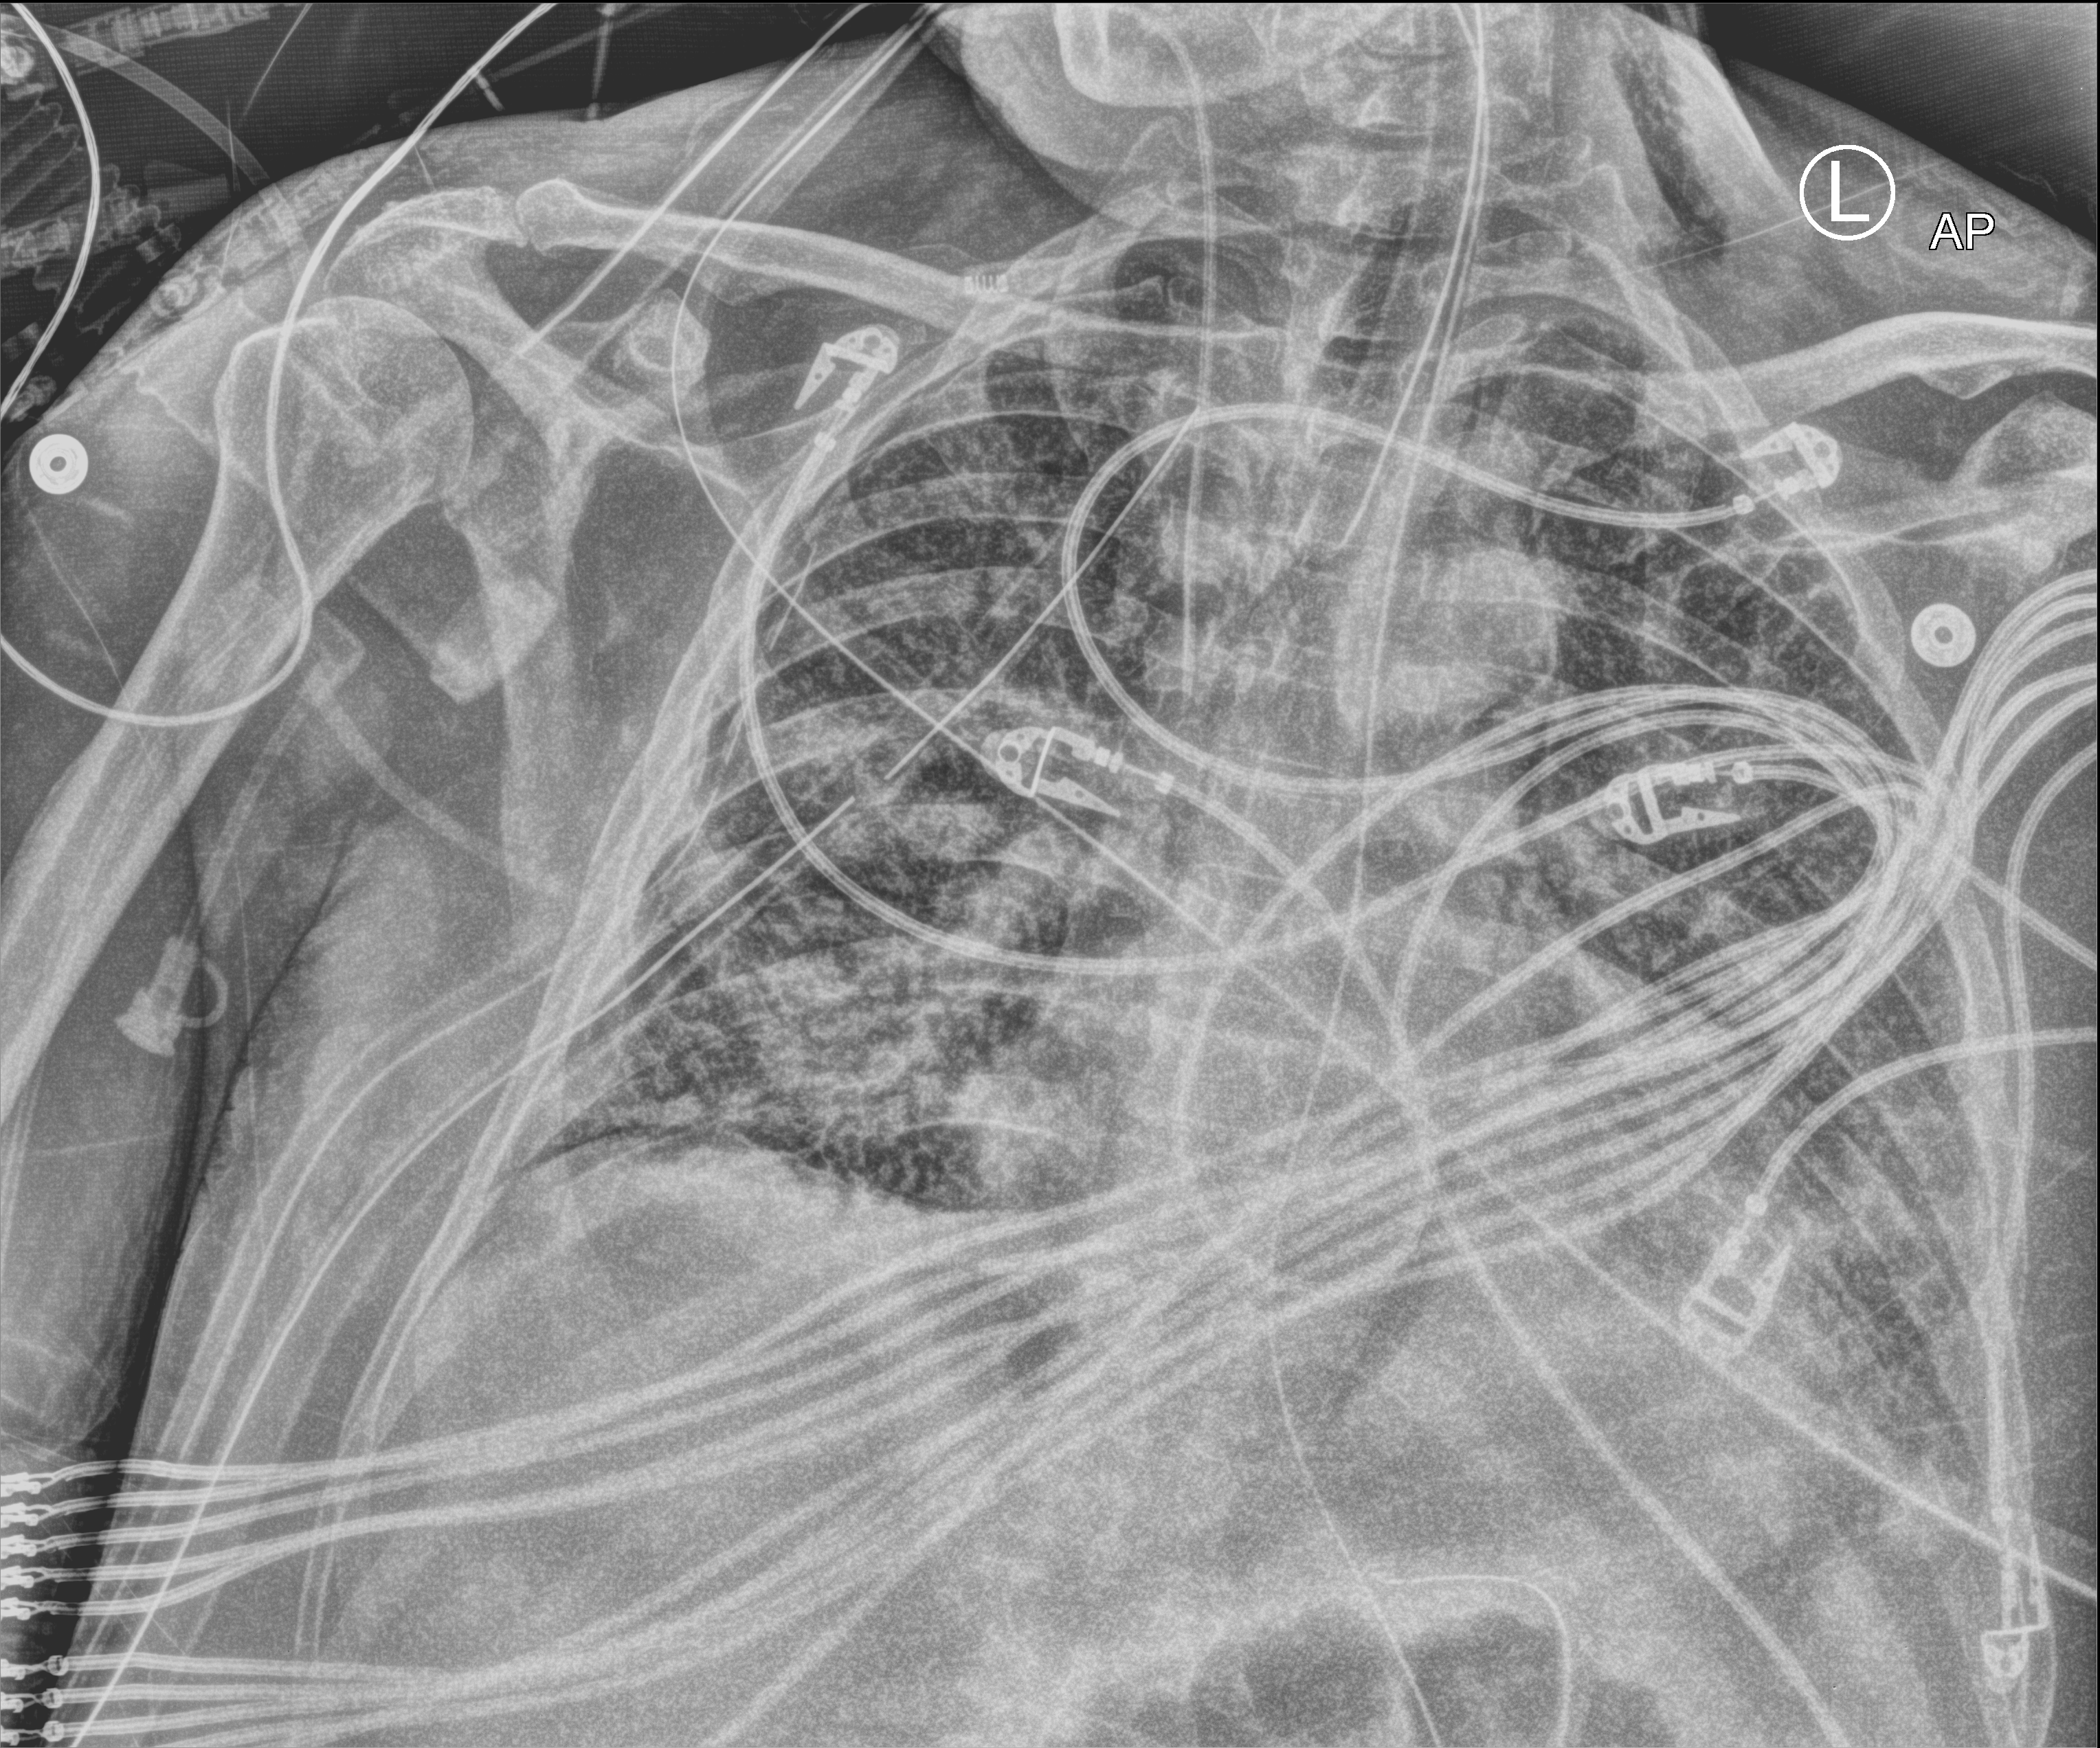
Portable chest radiograph; anteroposterior (AP) projection. Patient hospitalised with COVID-19; male, aged 60–74 years.
From the hospital-stay record, not from the radiograph (when in the stay this image was taken is not recorded):
- admitted to intensive care during this hospital stay: yes
- chronic kidney disease (admission record): no